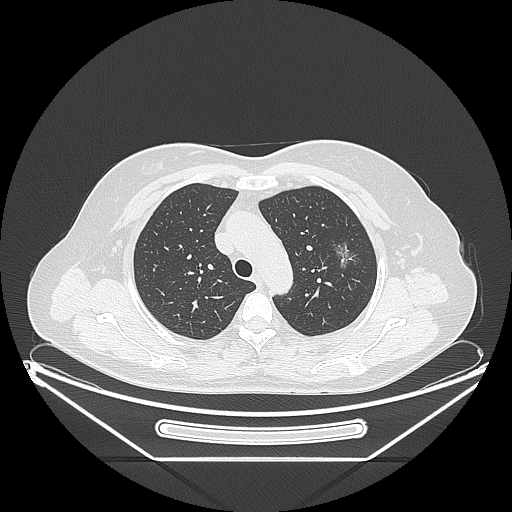
Chest CT, one axial slice; position 163 of 226 along the scan axis; reconstruction kernel LUNG; lung window (W 1500 / L -600 HU); 512 × 512 image matrix. Patient: female, 54 years. From the clinical record (not read from this slice): clinical TNM (as recorded): T1c N0 M0.
Structures marked on this image (rectangle marked by the reading radiologist):
- lung tumour (recorded histology: adenocarcinoma): bounding box [x1, y1, x2, y2] px = [324, 235, 365, 277]